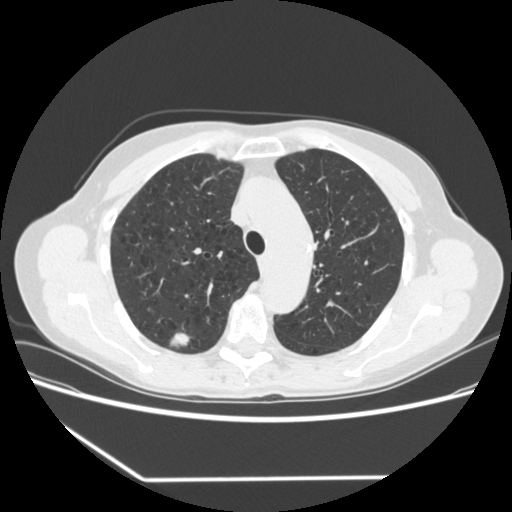
Low-dose screening chest CT, axial slice. Baseline annual screen. Lung window (W 1500 / L -600 HU). 1.25 mm slice thickness. 120 kVp. Slice 247 of 323 in the series. Female, age 67 years at enrolment. Current smoker at enrolment.
• Lesion marked by an expert reader, box from (x=154, y=322) to (x=199, y=356) px.
• The screening reader recorded 2 non-calcified nodules or masses ≥4 mm on this exam (right upper lobe, right lower lobe); which of them this box marks is not recorded.
• Official screen result: positive, change unspecified: nodule(s) >= 4 mm or enlarging nodule(s), mass(es), or other non-specific abnormalities suspicious for lung cancer.
• Lung cancer was diagnosed 29 days after this screen: adenocarcinoma, NOS, right upper lobe, moderately differentiated (G2), stage IA (AJCC 6th edition), 24 mm at pathology.